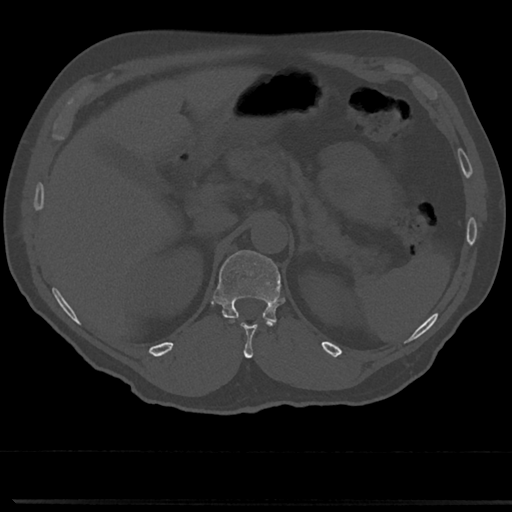
CT including the spine, one axial slice. Position 167 of 817 along the scan axis. Bone window (W 1800 / L 400 HU). 0.5 mm slice thickness. 512 × 512 image matrix, field of view 355 × 355 mm. Male patient, age 61 years. From the clinical record (not read from this slice): primary cancer: prostate.
Outlined on this slice (semi-automatic segmentation, software-assisted and operator-edited):
- T11 vertebra: bounding box <232,327,253,358> (left, top, right, bottom; pixels)
- T12 vertebra: <214,250,286,337>